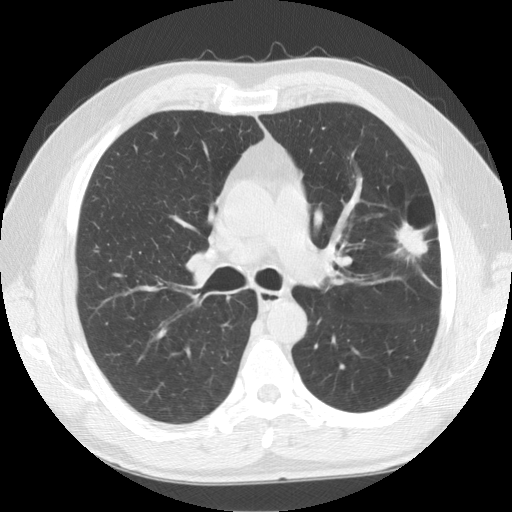
Chest CT (low-dose screening protocol), one axial image, first (baseline) screen, lung window (W 1500 / L -600 HU), 2.5 mm slice thickness, slice 50 of 141 in the series, 512 × 512 image matrix. Male, age 59 years at enrolment. Former smoker at enrolment.
• Expert-annotated lung lesion, box from (x=376, y=204) to (x=456, y=283) px.
• The exam's reader record, not a measurement of the box and not confirmed to be the same lesion: non-calcified nodule or mass ≥4 mm, left upper lobe, 23 × 23 mm, spiculated (stellate) margins, soft tissue attenuation.
• Later outcome: lung cancer diagnosed 28 days after this screen — squamous cell carcinoma, NOS, left upper lobe, moderately differentiated (G2), stage IA (AJCC 6th edition), 27 mm at pathology.